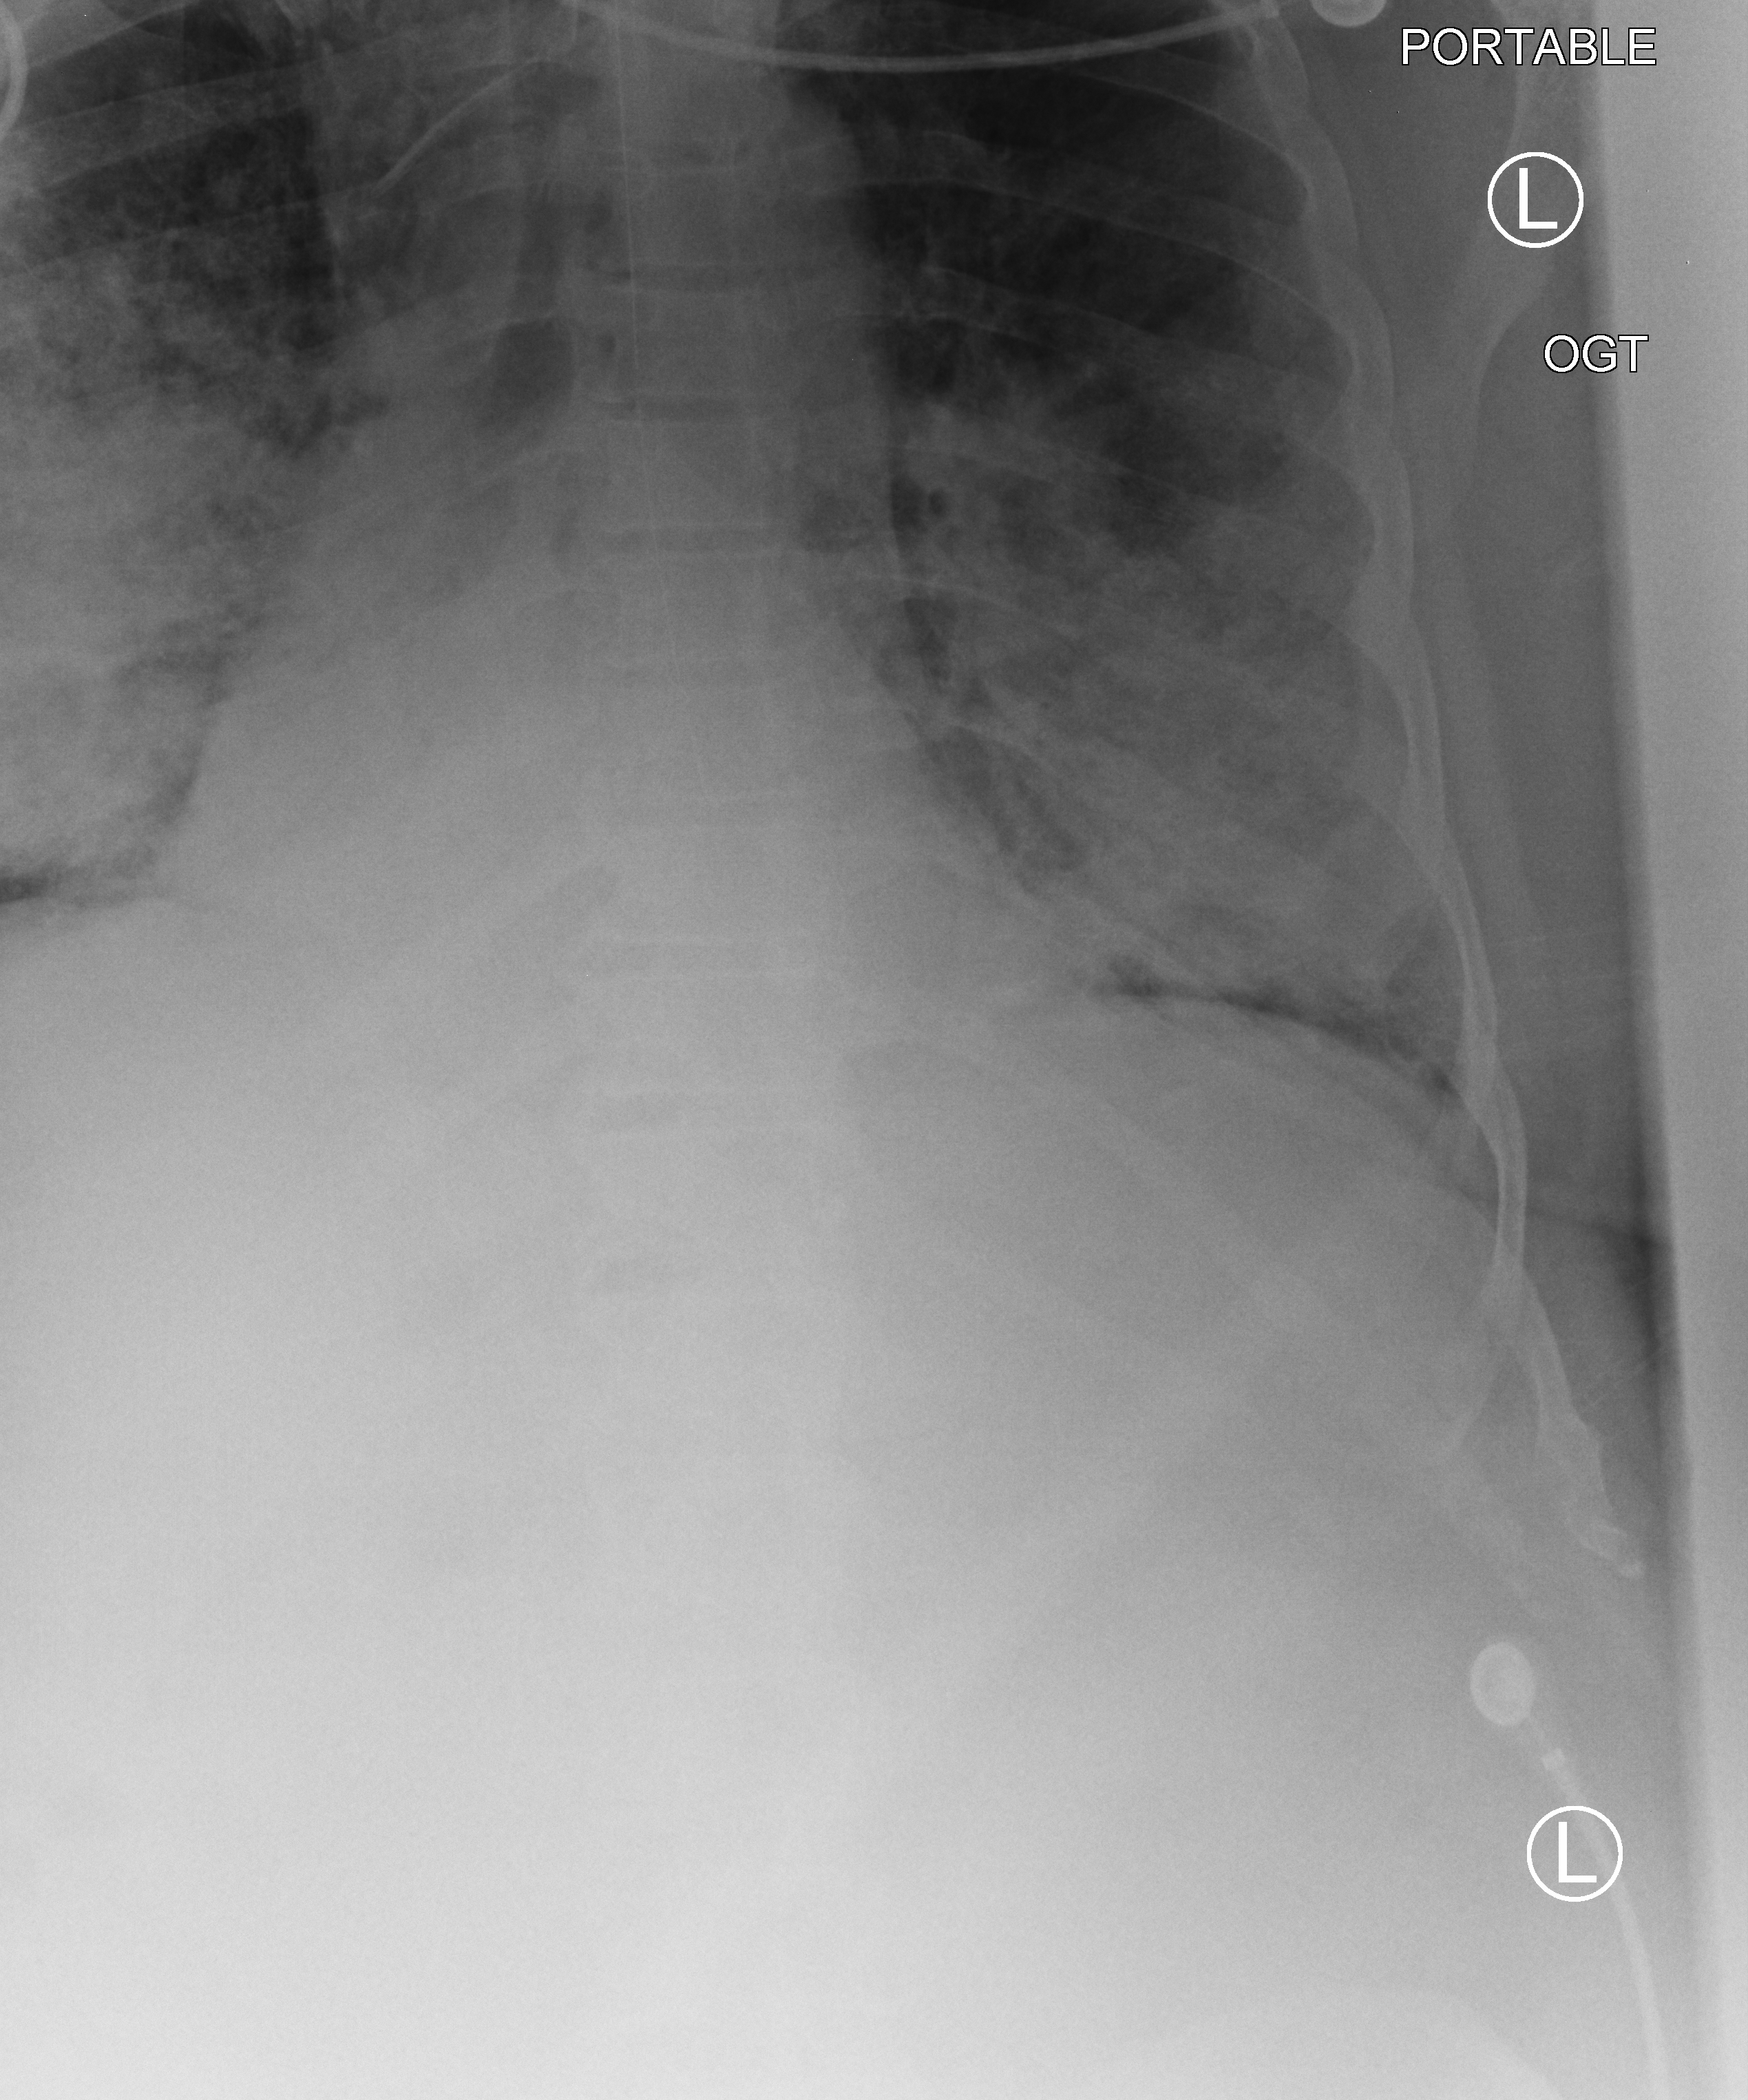
Bedside chest radiograph (computed radiography); anteroposterior (AP) projection. Patient hospitalised with COVID-19, aged 18–59 years.
From the hospital-stay record, not from the radiograph (when in the stay this image was taken is not recorded):
- smoking status (admission record): never
- COPD (admission record): no
- chronic kidney disease (admission record): no